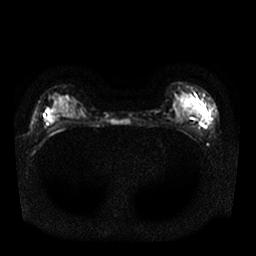
Breast MRI, one axial slice. Slice 12 of 25 in the series (ordered by position). Diffusion-weighted series; image 2 of 4 stored at this slice position (different b-values; order by instance number). 1.5 T. 4 mm slice thickness. 256 × 256 image matrix, field of view 340 × 340 mm. Female patient.
Outlined on this slice (expert manual segmentation):
- tumour on diffusion-weighted imaging: box from (x=199, y=111) to (x=206, y=121) px